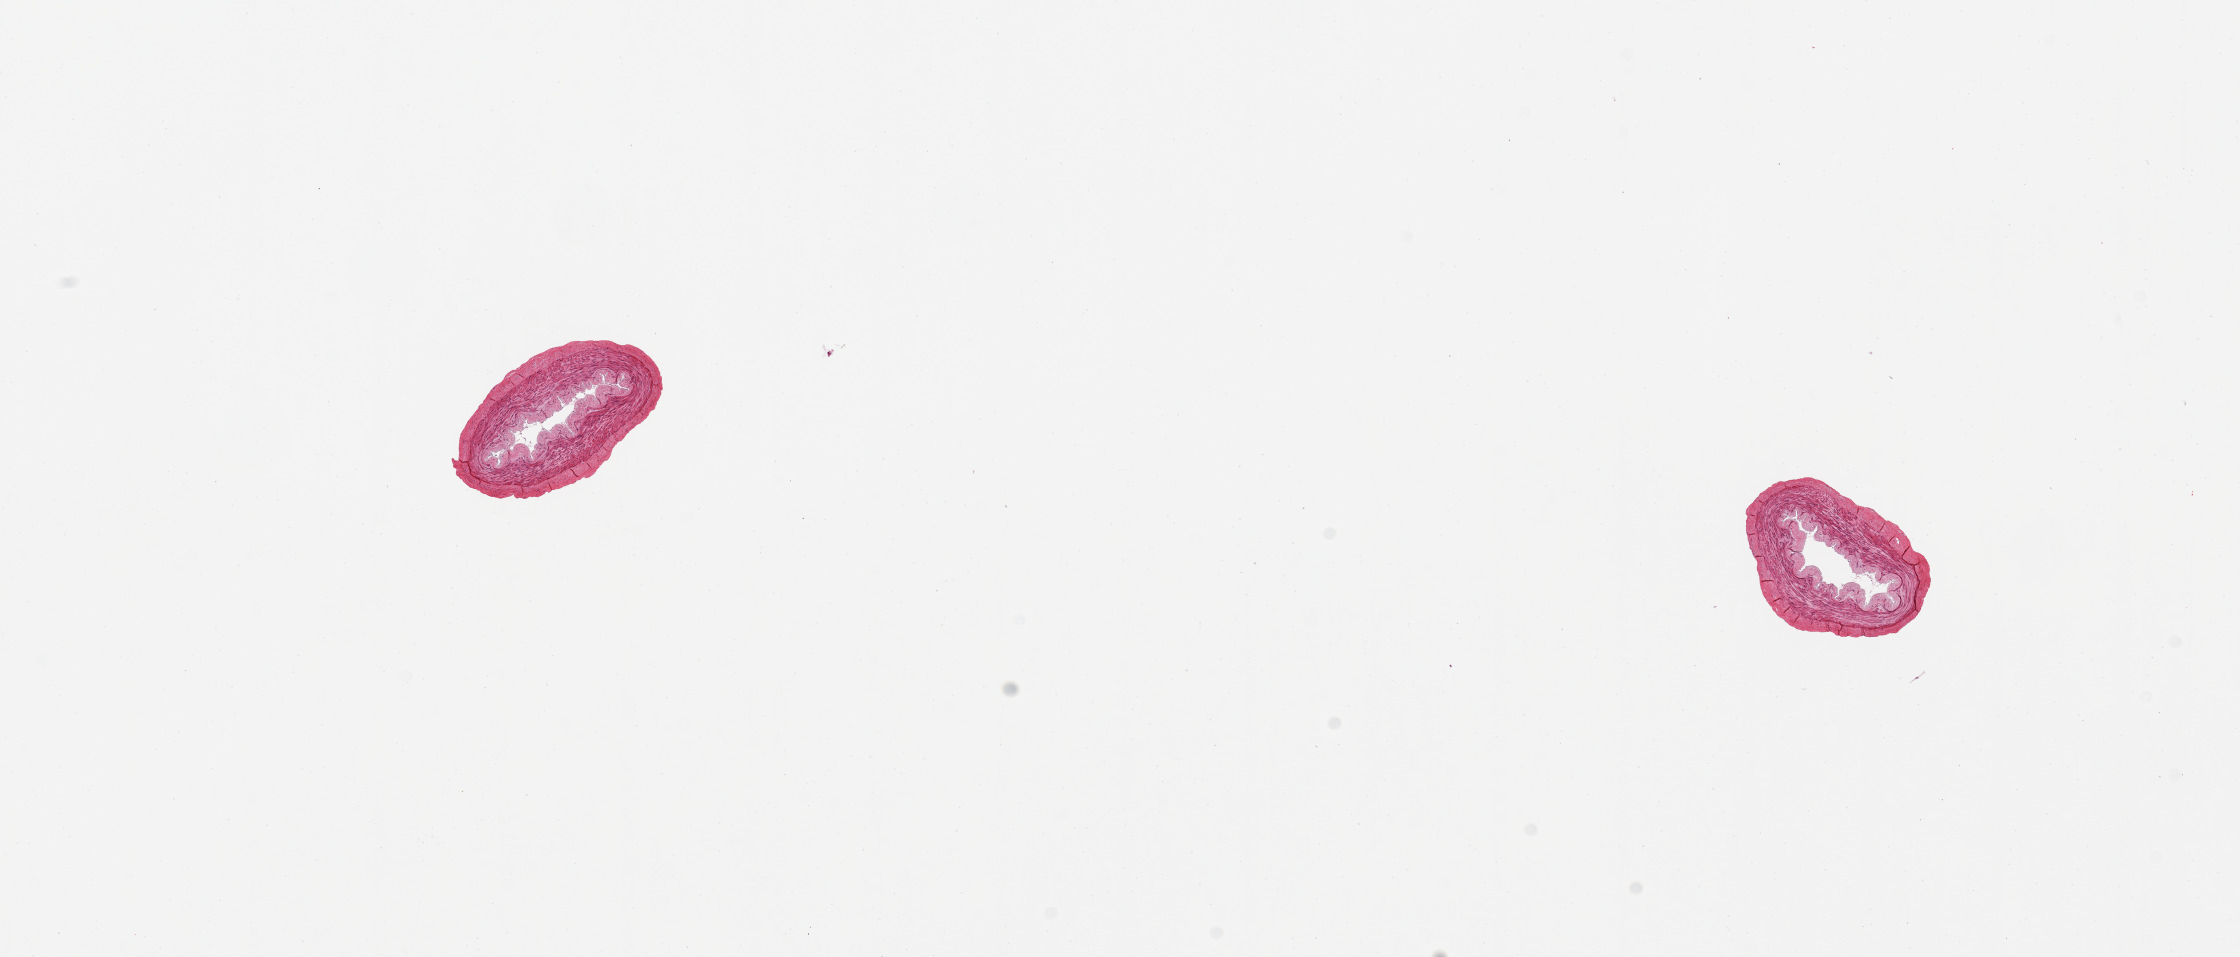
H&E whole-slide image, shown as a low-resolution overview of the whole scanned area (about 17.7 x 7.6 mm); PAXgene-fixed, paraffin-embedded tissue; target tissue: tibial artery; donor tissue sample. Female donor.
* reviewer comment on this tissue sample: 2 pieces, pristine specimens. No atherosis